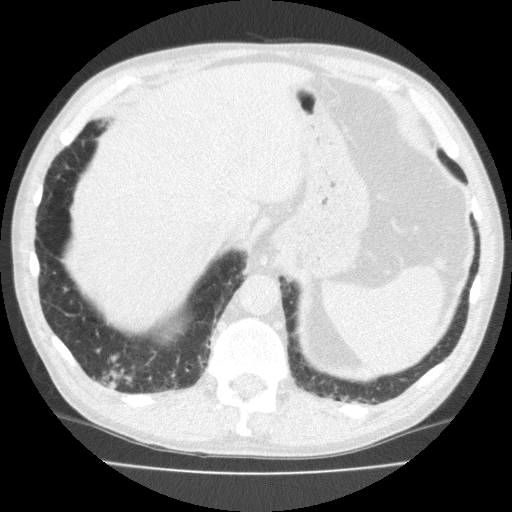
Low-dose screening chest CT, one axial slice. Position 45 of 195 along the scan axis. Reconstruction kernel FC10. 120 kVp. Lung window (W 1500 / L -600 HU). 512 × 512 image matrix, field of view 350 × 350 mm.
Outlined on this slice (expert manual segmentation):
- lesion 1 (tumor, lower lobe of right lung): bounding box <102,364,132,390> (left, top, right, bottom; pixels)